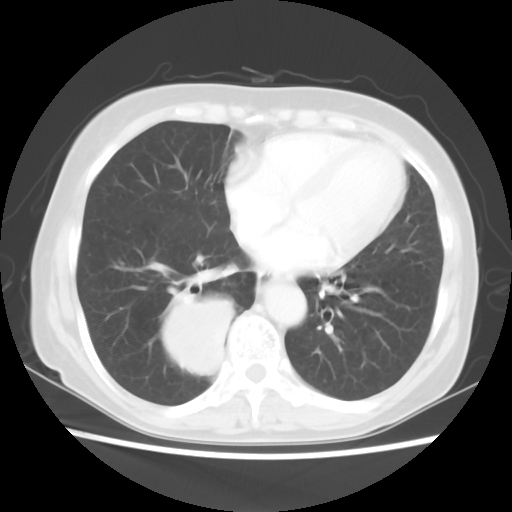
Chest CT, one axial slice; slice 21 of 56 in the series (ordered by position); lung window (W 1500 / L -600 HU); 5 mm slice thickness; 512 × 512 image matrix. Patient: female, 66 years. From the clinical record (not read from this slice): clinical TNM (as recorded): T2 N3 M0.
Annotated regions visible in this slice (bounding box drawn by a radiologist):
- lung tumour (recorded histology: small cell carcinoma): box from (x=160, y=298) to (x=242, y=378) px